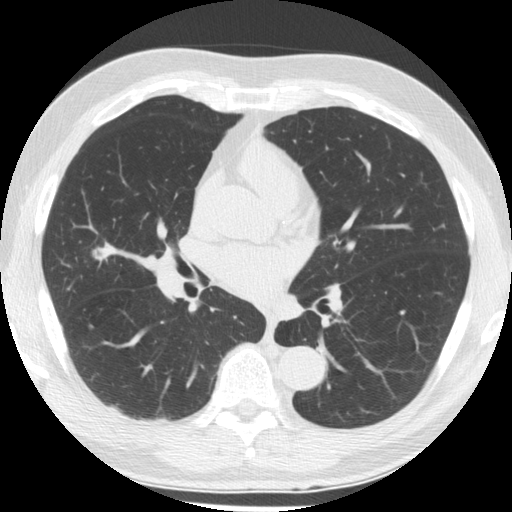
Low-dose screening chest CT, one axial slice; slice 97 of 176 in the series (ordered by position); reconstruction kernel STANDARD; 120 kVp; lung window (W 1500 / L -600 HU); 512 × 512 image matrix, field of view 348 × 348 mm.
Outlined on this slice (expert manual segmentation):
- lesion 1 (tumor, middle lobe of right lung): bounding box <92,247,111,266> (left, top, right, bottom; pixels)